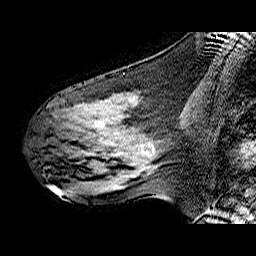
Breast MRI (dynamic contrast-enhanced), one sagittal slice; slice 27 of 60 in the series (ordered by position); dynamic contrast-enhanced series, time point 2 of 6 at this slice position (early post-contrast); 1.5 T; TE 6.3 ms, TR 32.9 ms; 4 mm slice thickness; 256 × 256 image matrix, field of view 200 × 200 mm. Female patient. Case-level facts recorded for this patient, not image findings: setting: breast cancer imaged before/during neoadjuvant chemotherapy; receptor status: HER2-positive.
Structures marked on this image (semi-automatic segmentation, software-assisted and operator-edited):
- analysis volume of interest (the breast-tissue region the enhancement analysis was run in; not a lesion): bounding box (x1, y1, x2, y2) in pixels: (49, 93, 172, 173)
- tumour enhancement mask (voxels above the 100 % enhancement threshold inside the analysis volume of interest): (145, 152, 148, 154)